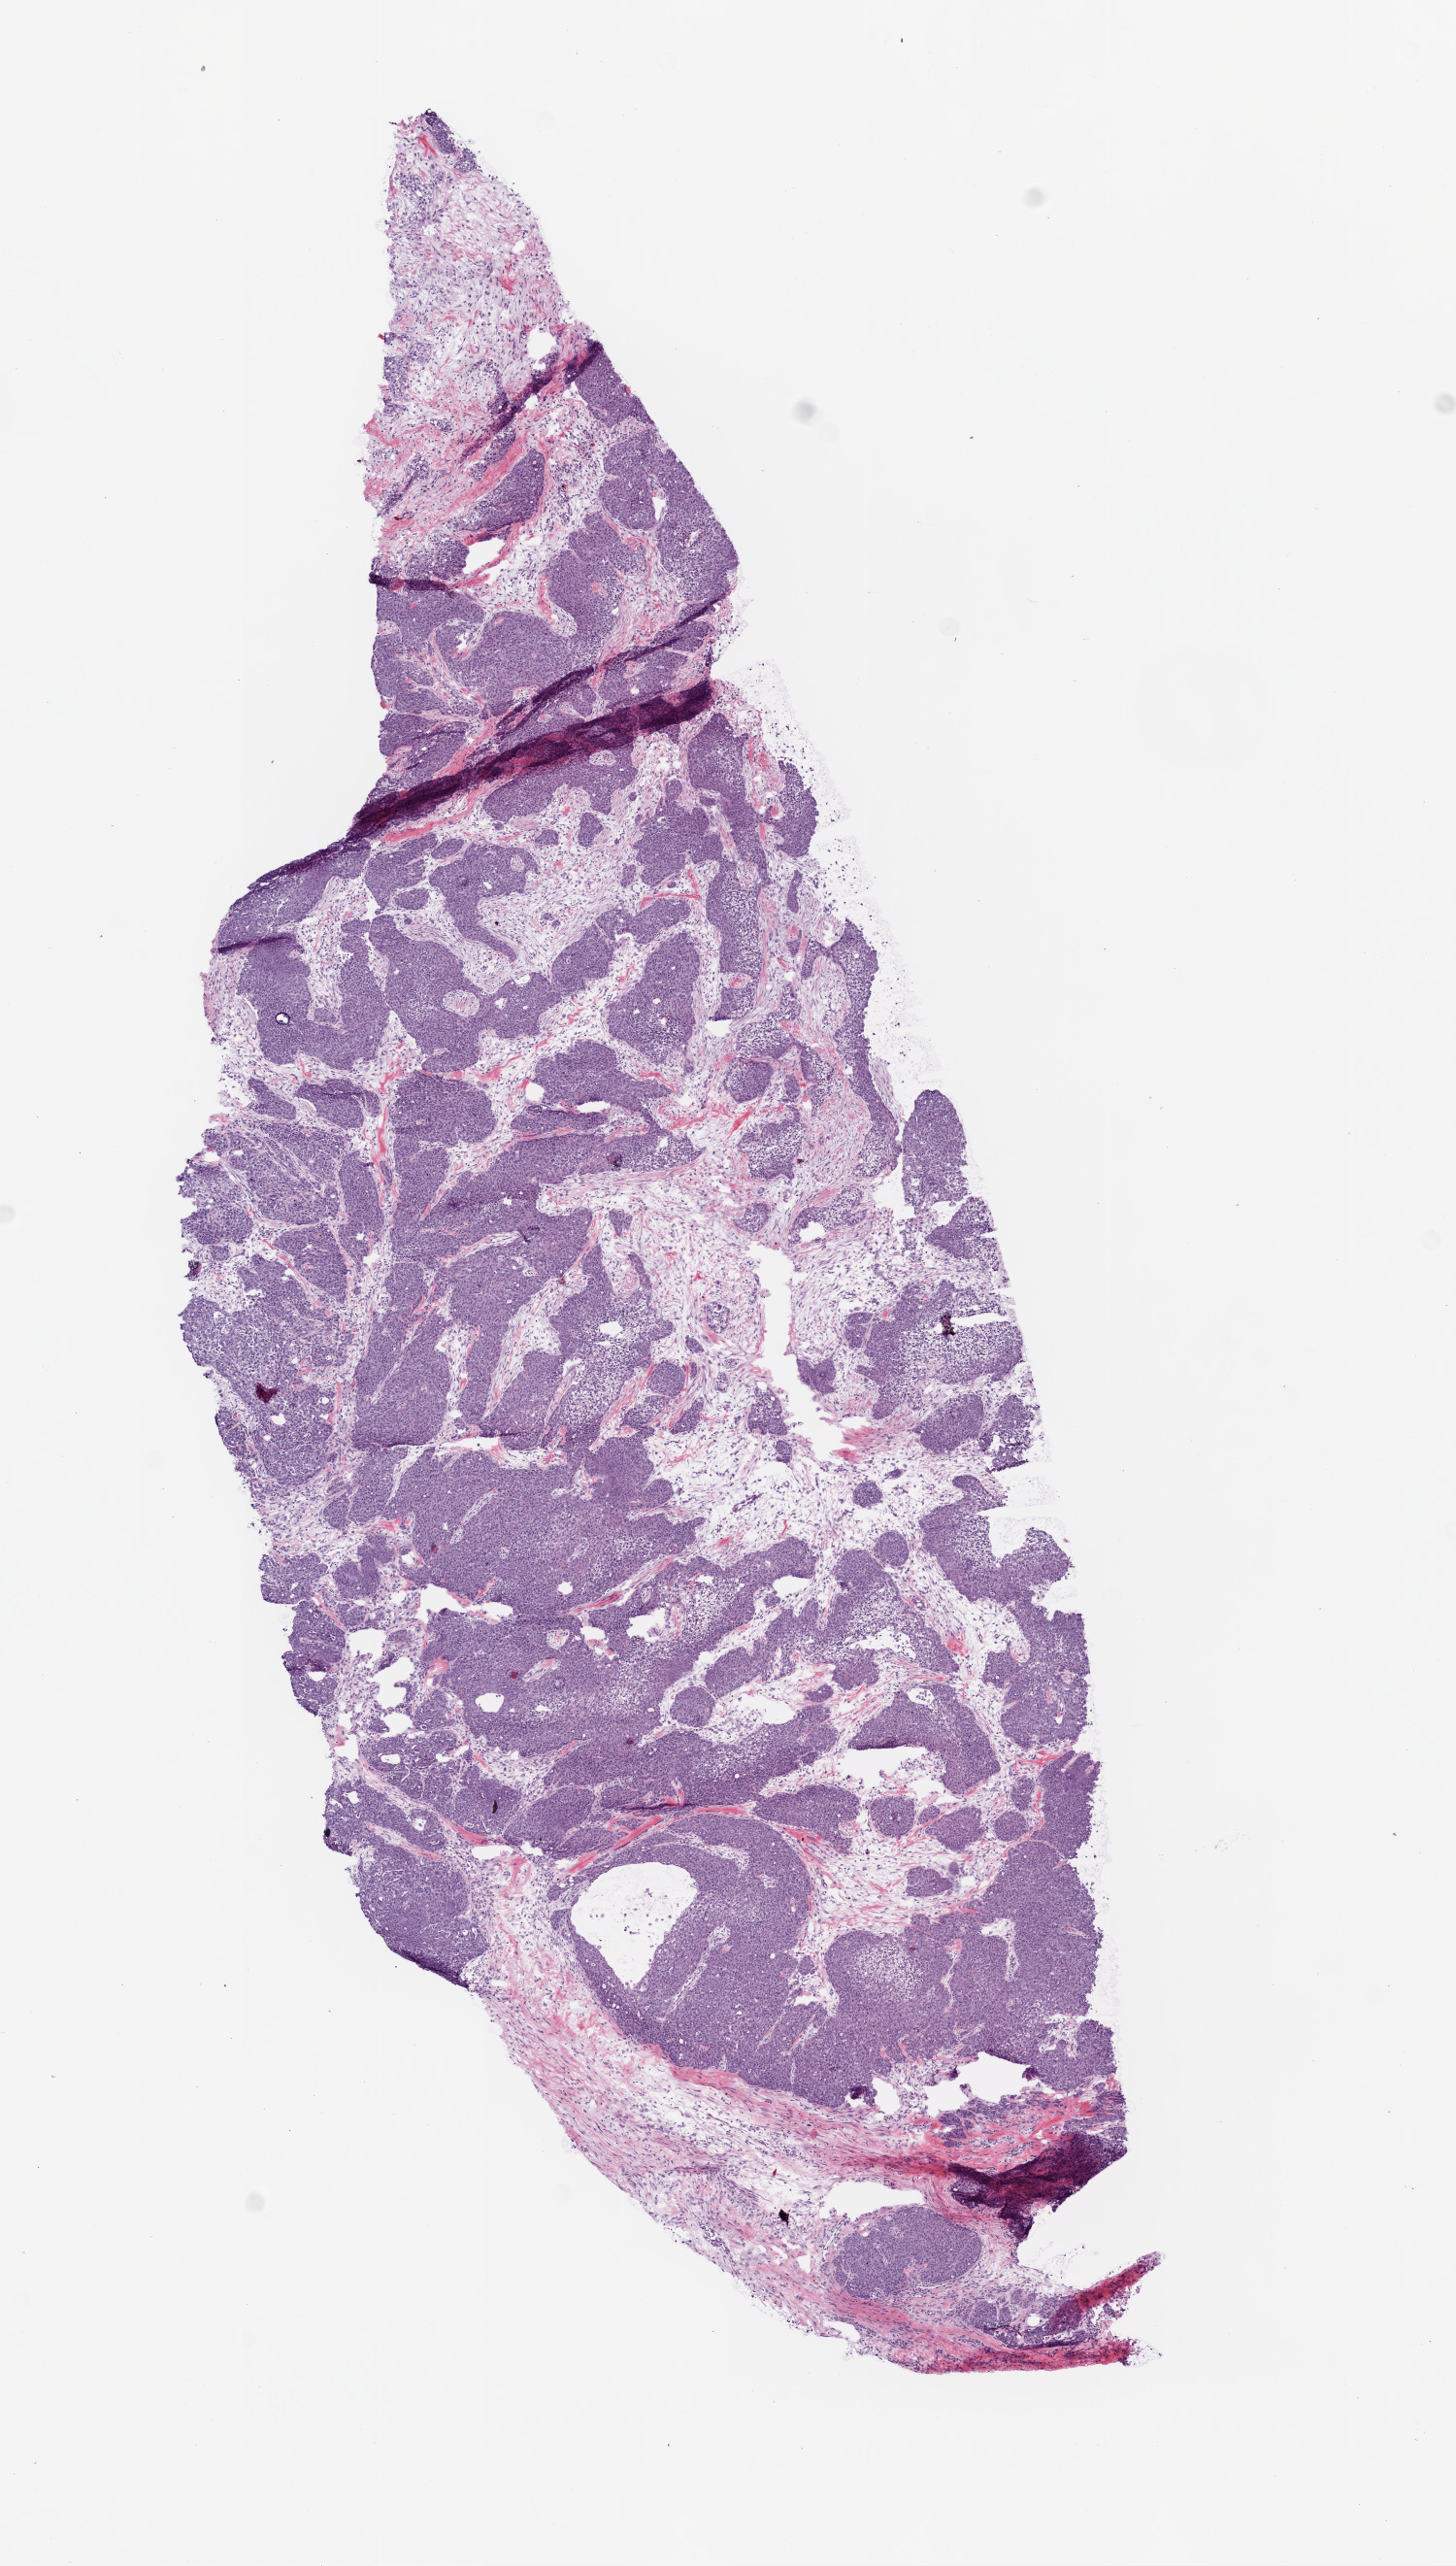
H&E whole-slide image — shown as a low-resolution overview of the whole scanned area (about 6.0 x 10.6 mm). Frozen section. Ovary, primary tumour sample. Female patient; age at initial diagnosis 52 years. Histologic grade: G3 (poorly differentiated). Pathologist review of this section (percent, as recorded): tumour cells 95%, tumour nuclei 95%, normal cells 0%, stromal cells 5%, necrosis 0%.
Histologic diagnosis: Serous cystadenocarcinoma, NOS. FIGO stage: IIIC.